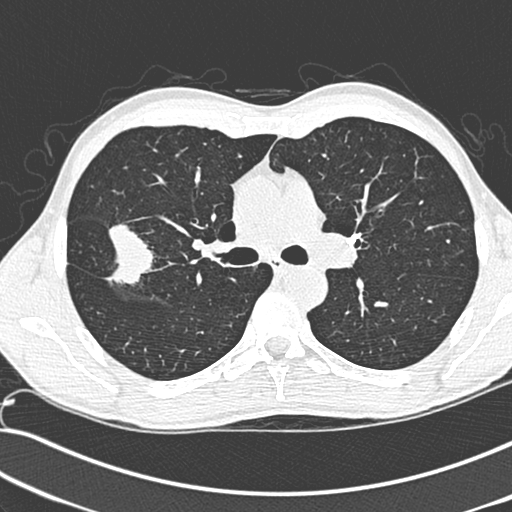
Low-dose screening chest CT, one axial slice. Slice 189 of 281 in the series (ordered by position). 120 kVp. Lung window (W 1500 / L -600 HU). 1.3 mm slice thickness. 512 × 512 image matrix, field of view 341 × 341 mm.
Structures marked on this image (outlined manually by an expert reader):
- lesion 1 (tumor, upper lobe of right lung): bounding box <107,224,154,285> (left, top, right, bottom; pixels)